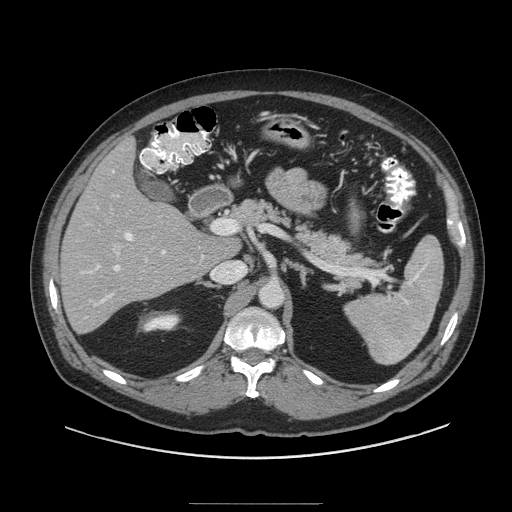
Contrast-enhanced abdominal CT (liver protocol), one axial slice; slice 54 of 91 in the series (ordered by position); reconstruction kernel STANDARD; 140 kVp; soft-tissue window (W 400 / L 40 HU); 512 × 512 image matrix, field of view 440 × 440 mm. From the clinical record (not read from this slice): diagnosis: hepatocellular carcinoma (patient treated with transarterial chemoembolisation; whether this scan precedes or follows treatment is not stated here); TNM stage (as recorded): Stage-I; Child-Pugh class: A; tumour nodularity: uninodular; tumour size: 4 cm.
Annotated regions visible in this slice (semi-automatically segmented with operator editing):
- liver parenchyma outside the tumour (the mass and vessels are separate outlines, so this box may not span the whole liver): bounding box (x1, y1, x2, y2) in pixels: (60, 138, 226, 332)
- liver vessels: (82, 170, 204, 306)